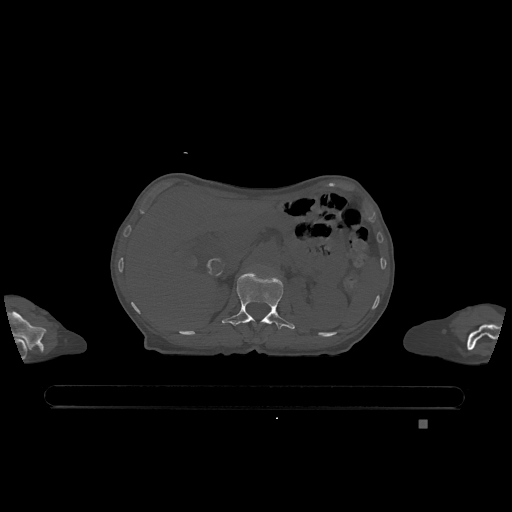
CT including the spine, one axial slice. Position 475 of 1317 along the scan axis. Bone window (W 1800 / L 400 HU). 0.5 mm slice thickness. 512 × 512 image matrix, field of view 500 × 500 mm. Female patient, age 74 years. From the clinical record (not read from this slice): primary cancer: lung; vertebrae with lytic lesions (as recorded): T1, T4, T5, T6, L4, L5.
Annotated regions visible in this slice (semi-automatically segmented with operator editing):
- L1 vertebra: bounding box [x1, y1, x2, y2] px = [222, 272, 295, 329]